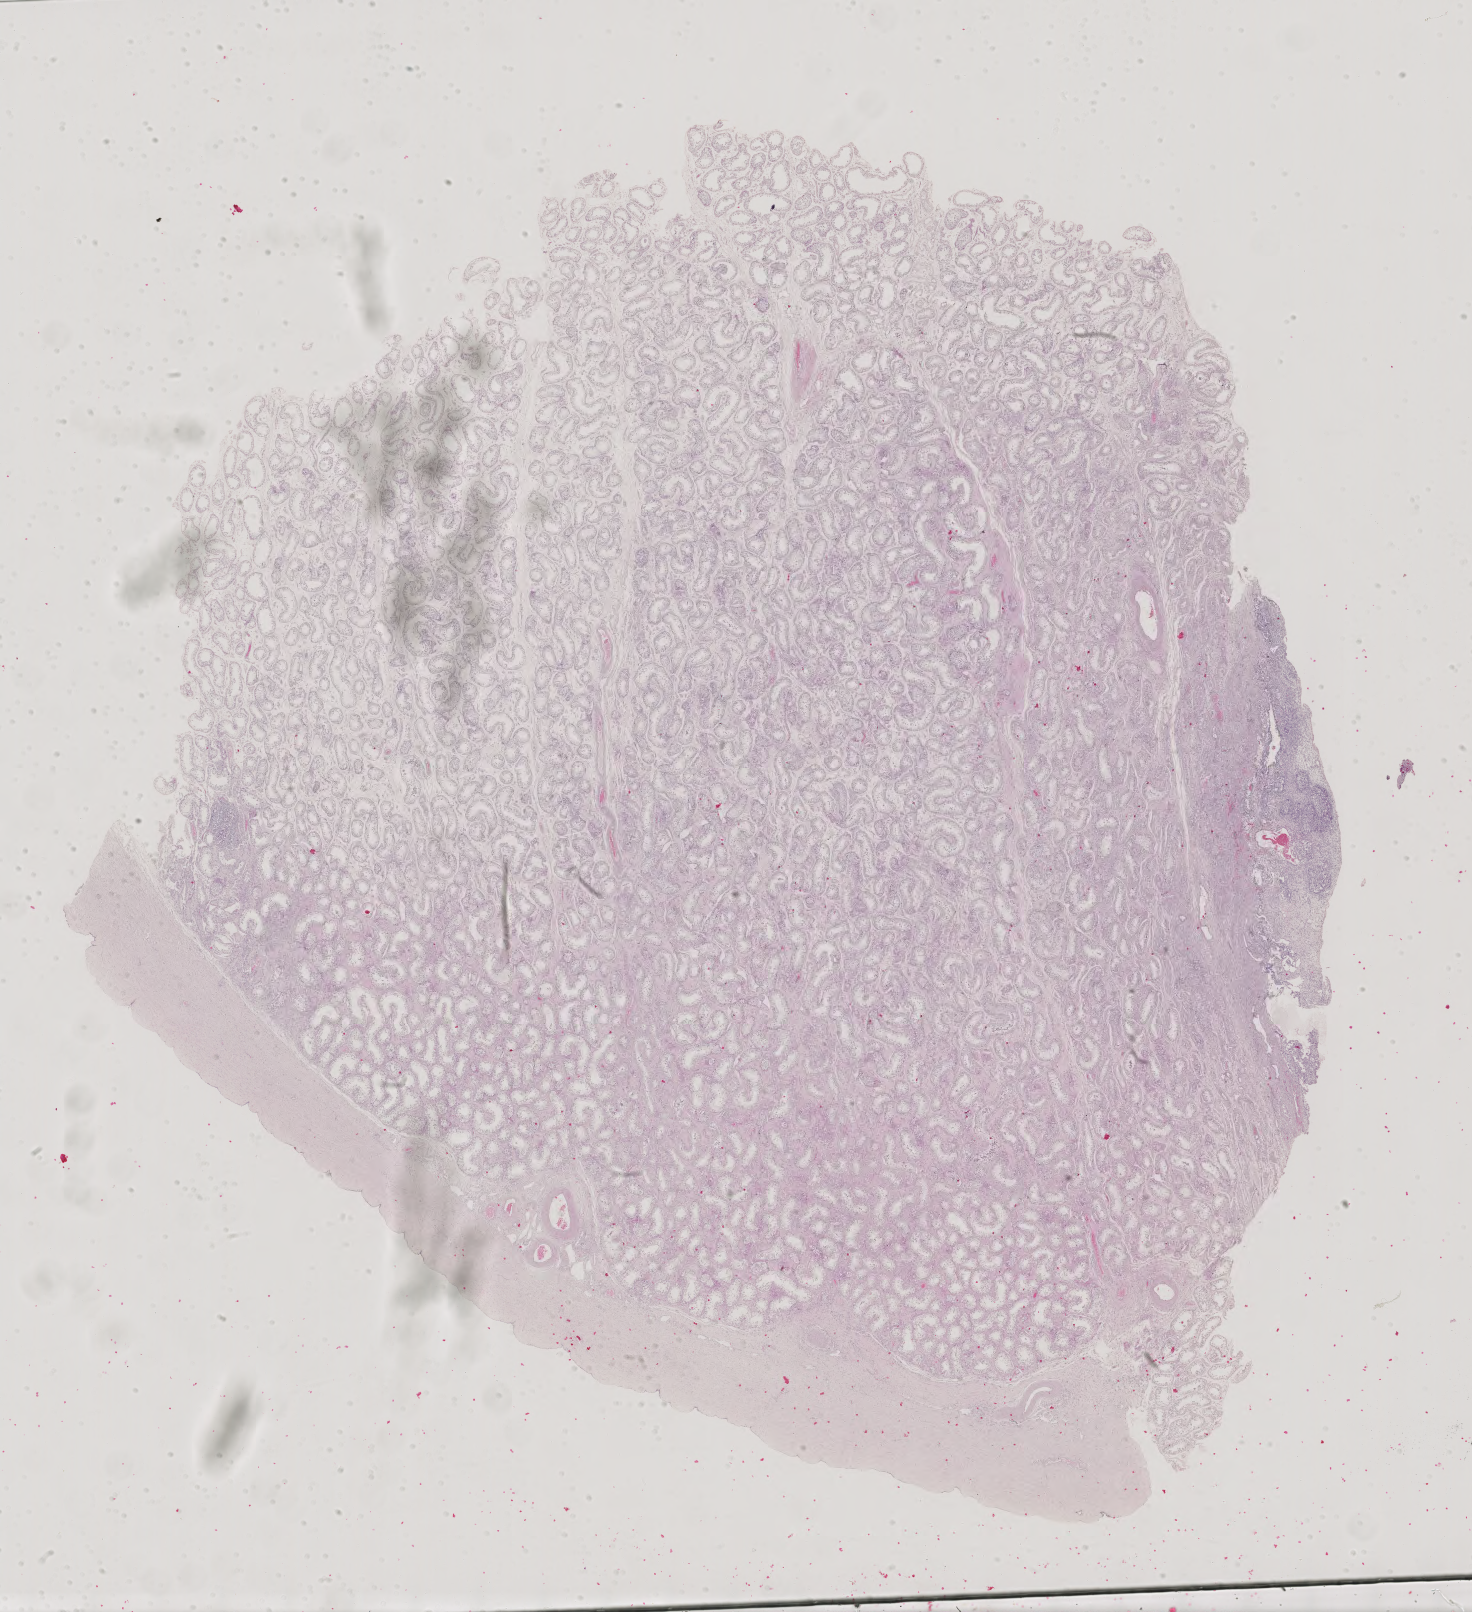
H&E-stained whole-slide image, low-resolution overview of the scanned area, about 21.5 x 23.5 mm (slide scanned at 40x). Formalin-fixed paraffin-embedded (FFPE) diagnostic section. Primary tumour sample from the testis. Male patient; age at initial diagnosis 33 years.
• AJCC pathologic stage: IS (6th edition)
• histologic diagnosis: Mixed germ cell tumor